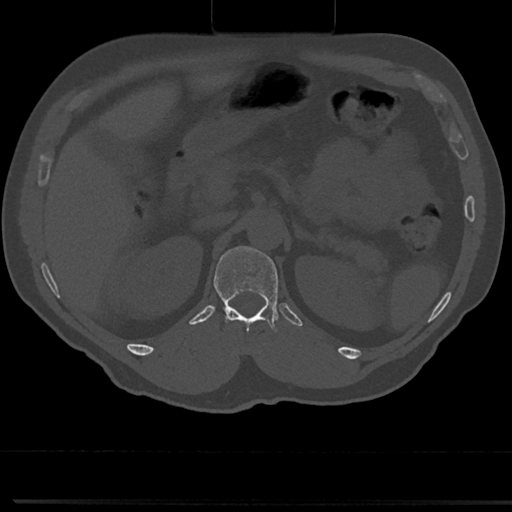
CT including the spine, one axial slice. Position 141 of 817 along the scan axis. Reconstruction kernel Br40s/3. 120 kVp. Bone window (W 1800 / L 400 HU). 0.5 mm slice thickness. 512 × 512 image matrix, field of view 355 × 355 mm. Male patient, age 61 years. From the clinical record (not read from this slice): primary cancer: prostate.
Structures marked on this image (semi-automatically segmented with operator editing):
- T12 vertebra: bounding box (x1, y1, x2, y2) in pixels: (211, 253, 282, 356)